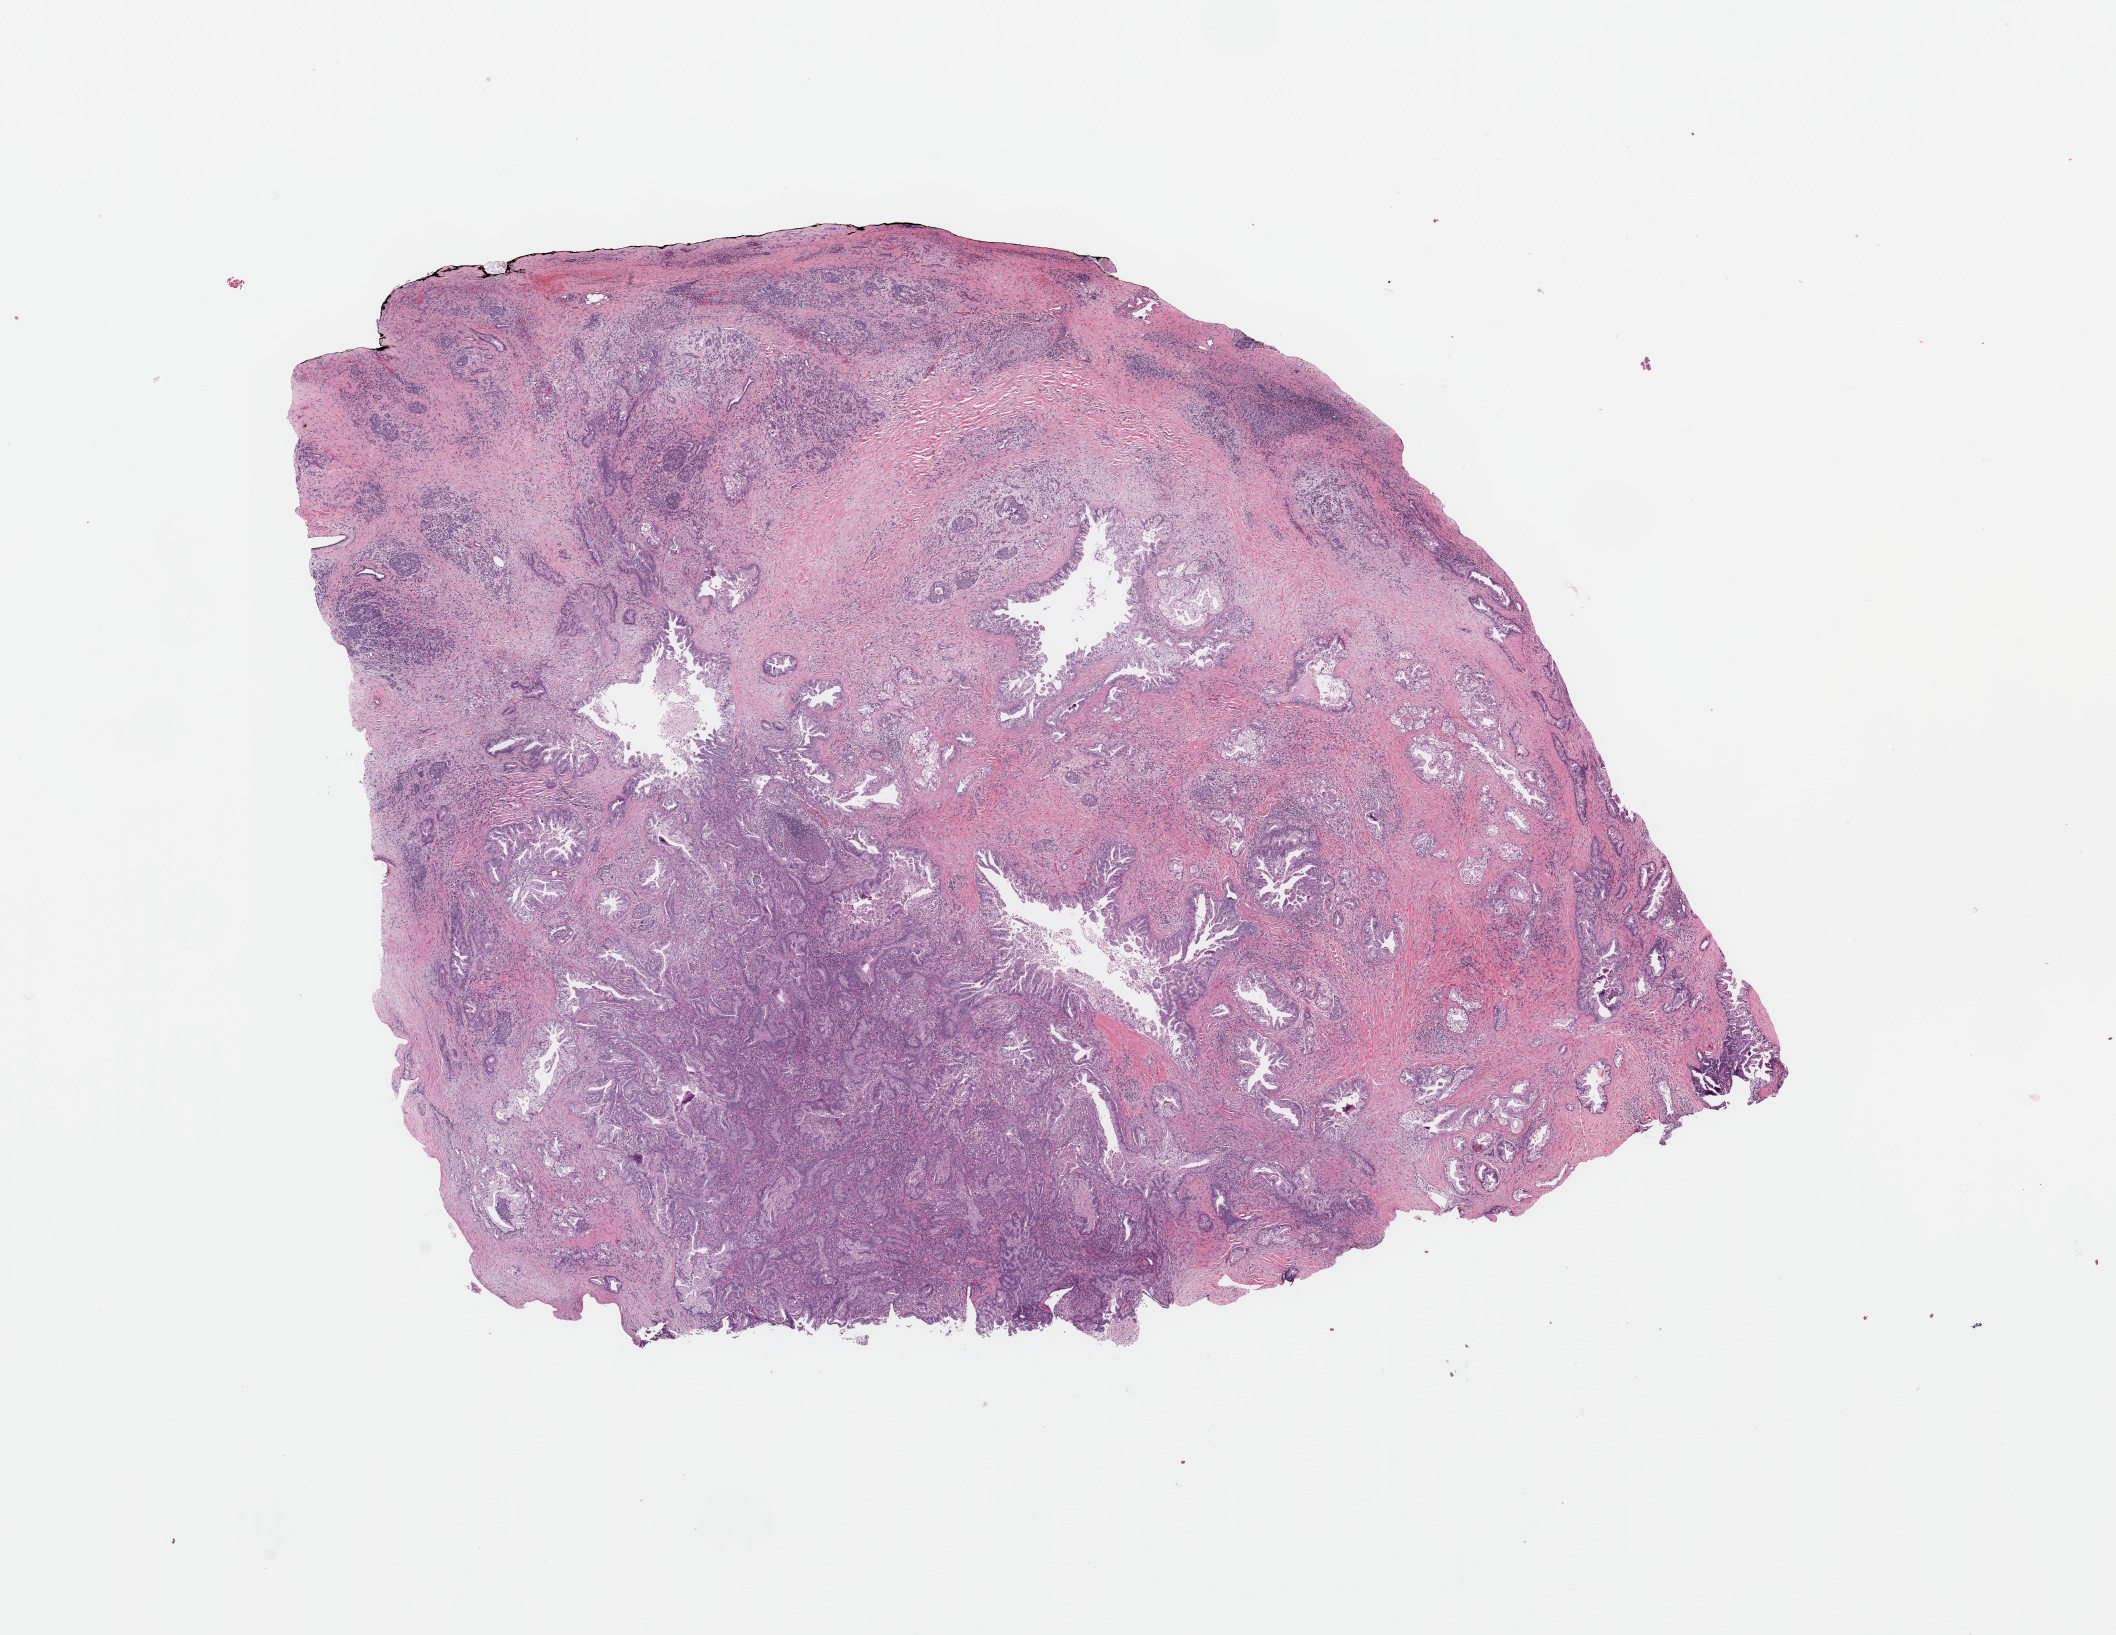
H&E whole-slide image — whole scanned area (about 16.7 x 12.9 mm, slide scanned at 20x) shown as a low-resolution overview. Tumour tissue sample, sampled site: pancreas. Patient: female, age 38 years. Composition of this section per pathologist review: tumour nuclei 40%, necrosis 2%.
Histologic diagnosis: Infiltrating duct carcinoma, NOS.